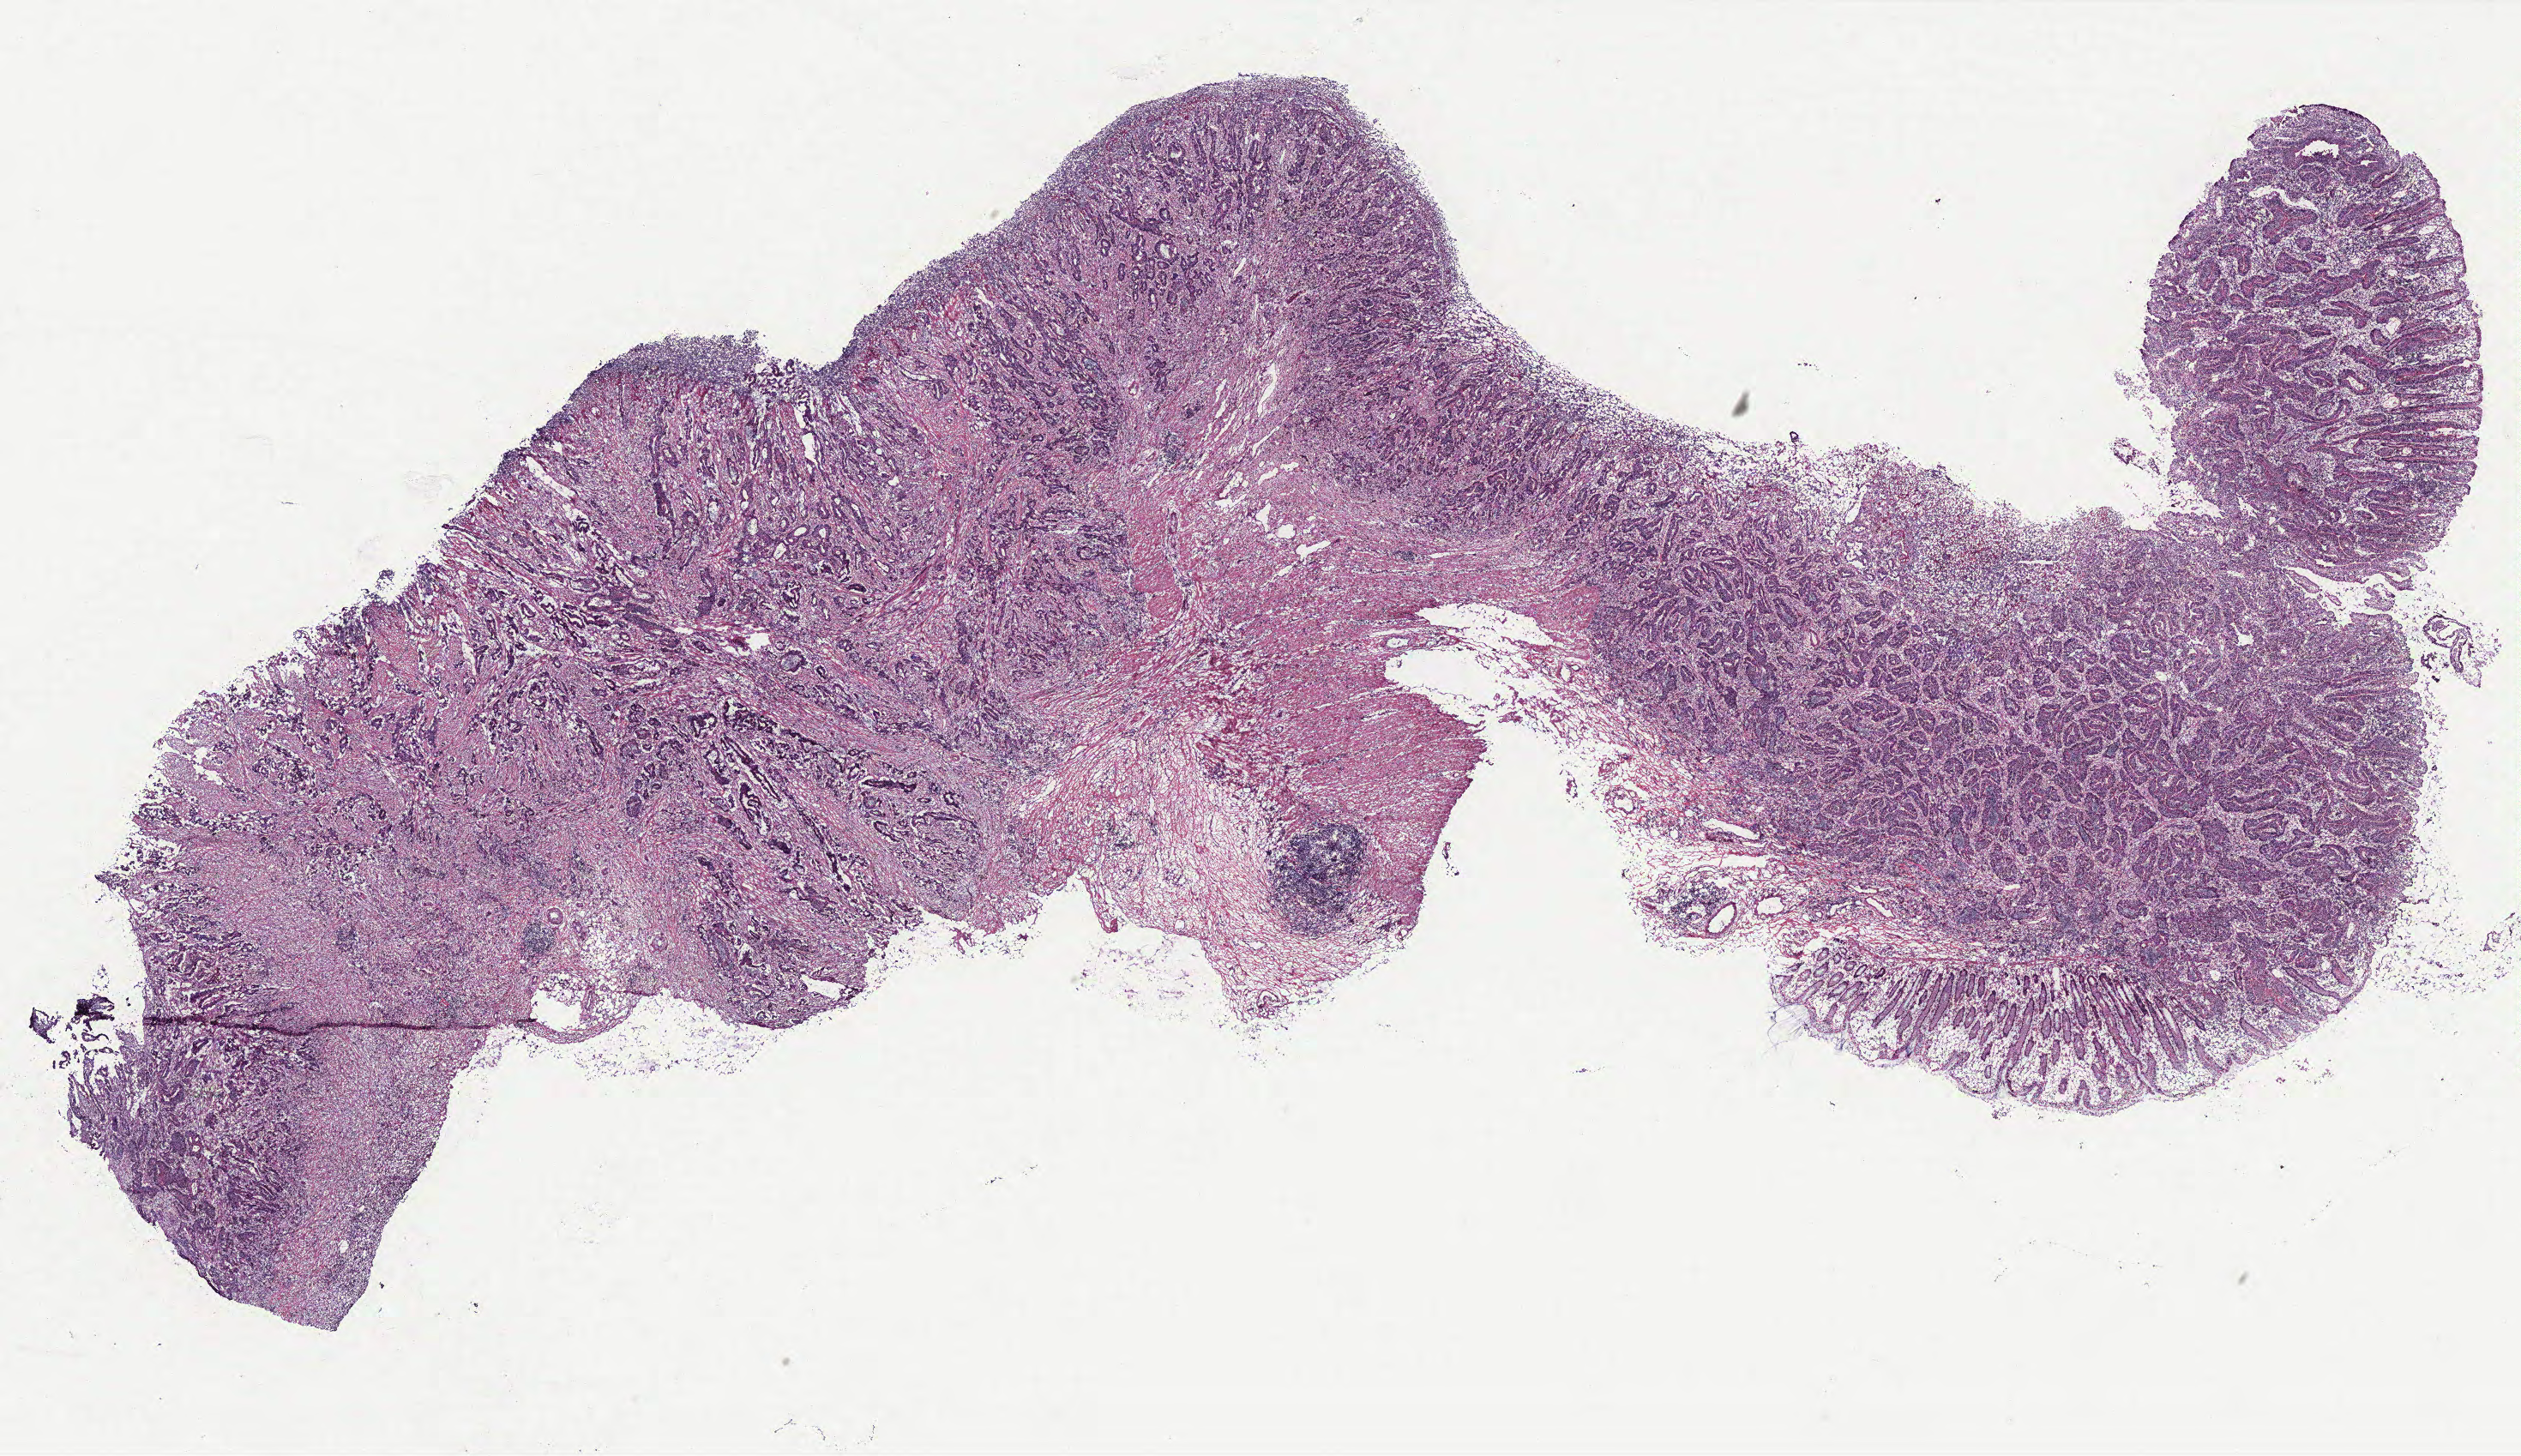
Digitized Hematoxylin and eosin (H&E) stained tissue section (whole slide), a low-resolution overview of the entire scanned area, about 23.5 x 13.6 mm (acquisition: 40x scan). Tumour tissue sample, colon. Female, 47 y/o.
- AJCC pathologic stage: IIA
- histologic diagnosis: Adenocarcinoma, NOS
- primary tumour site (as recorded): colon